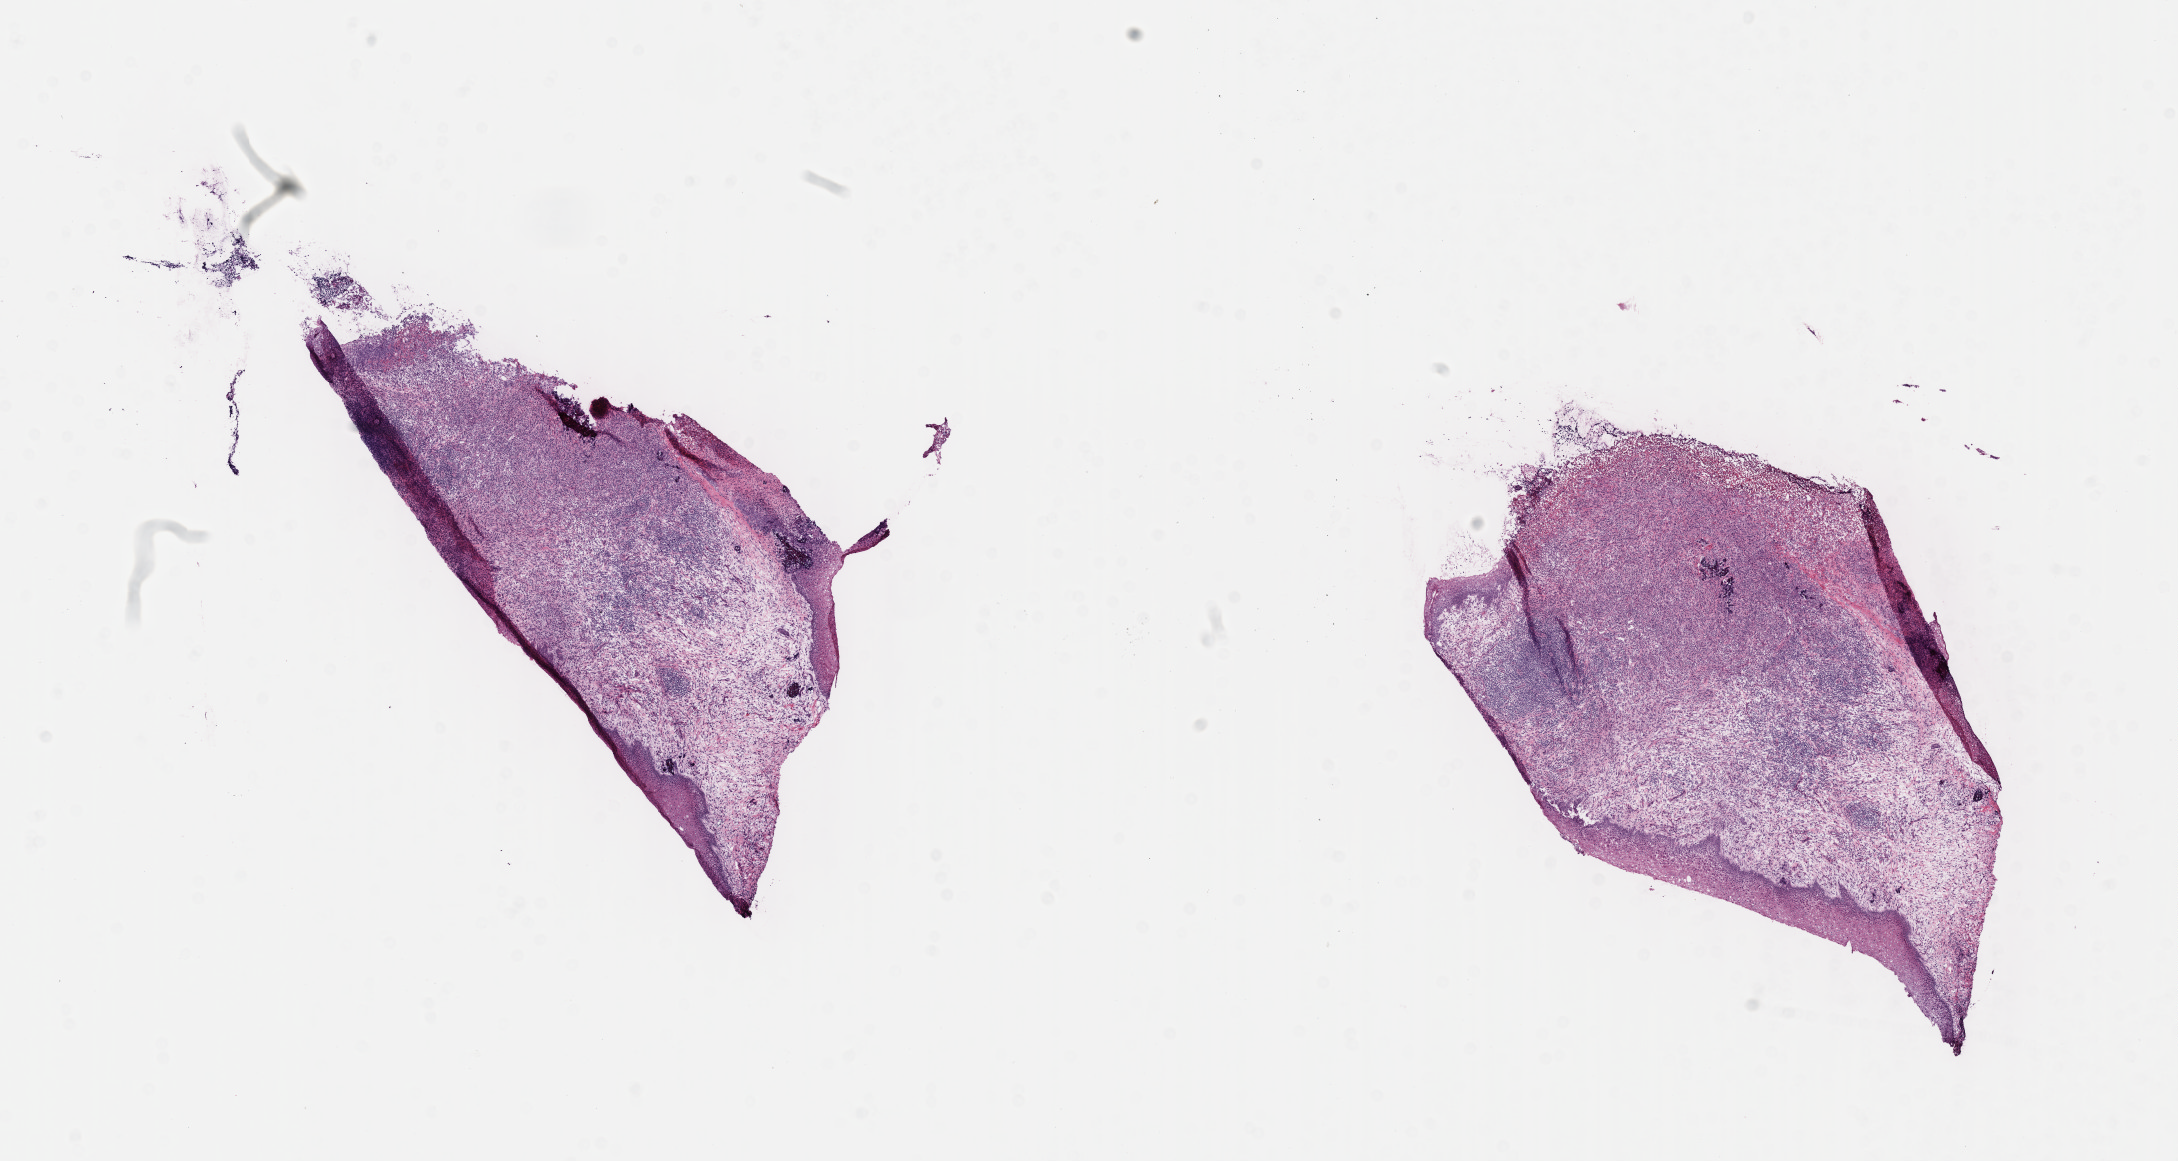
Haematoxylin and eosin whole-slide image — low-resolution overview of the scanned area, about 17.6 x 9.4 mm, frozen section (tissue freezing medium), primary tumor, site: cranium. Patient: female, age at initial diagnosis 6 years. Composition of this section per pathologist review: tumor cells 40%, tumor nuclei 80%, stromal cells 45%, necrosis 5%, normal cells 10%. Infiltration values recorded for this section: lymphocyte infiltration 20%, monocyte infiltration 20%, neutrophil infiltration 20%.
- Ann Arbor stage (patient): Stage IV
- section: top of the tissue portion
- diagnosis: Burkitt lymphoma, NOS